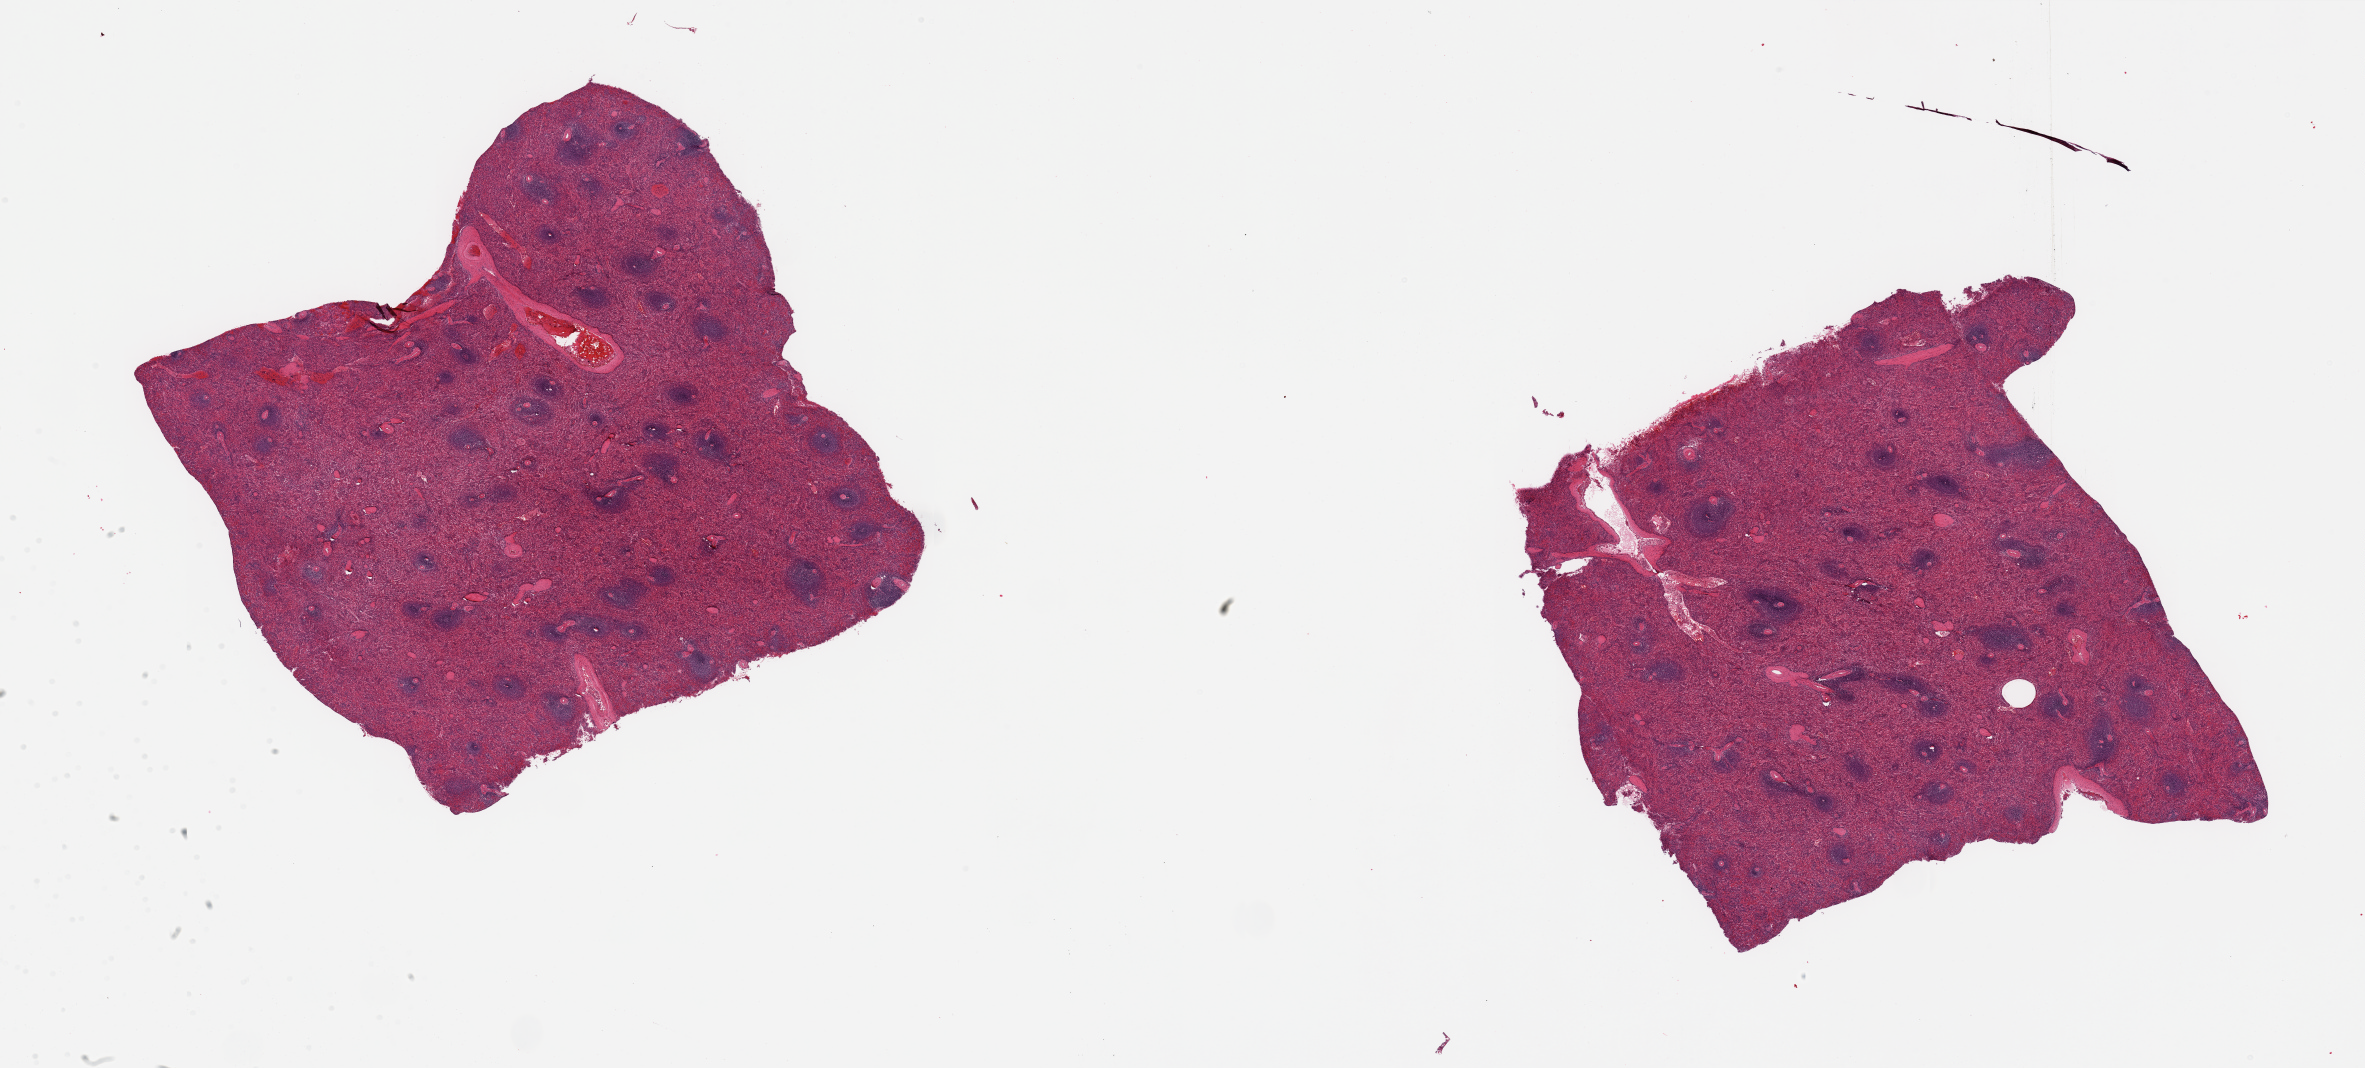
Digitized haematoxylin and eosin-stained section — low-resolution overview of the scanned area, about 37.4 x 16.9 mm; PAXgene-fixed paraffin-embedded (PFPE) section; target tissue: spleen; donor tissue sample.
Pathologist's review note for this sample: 2 pieces, no abnormalities.